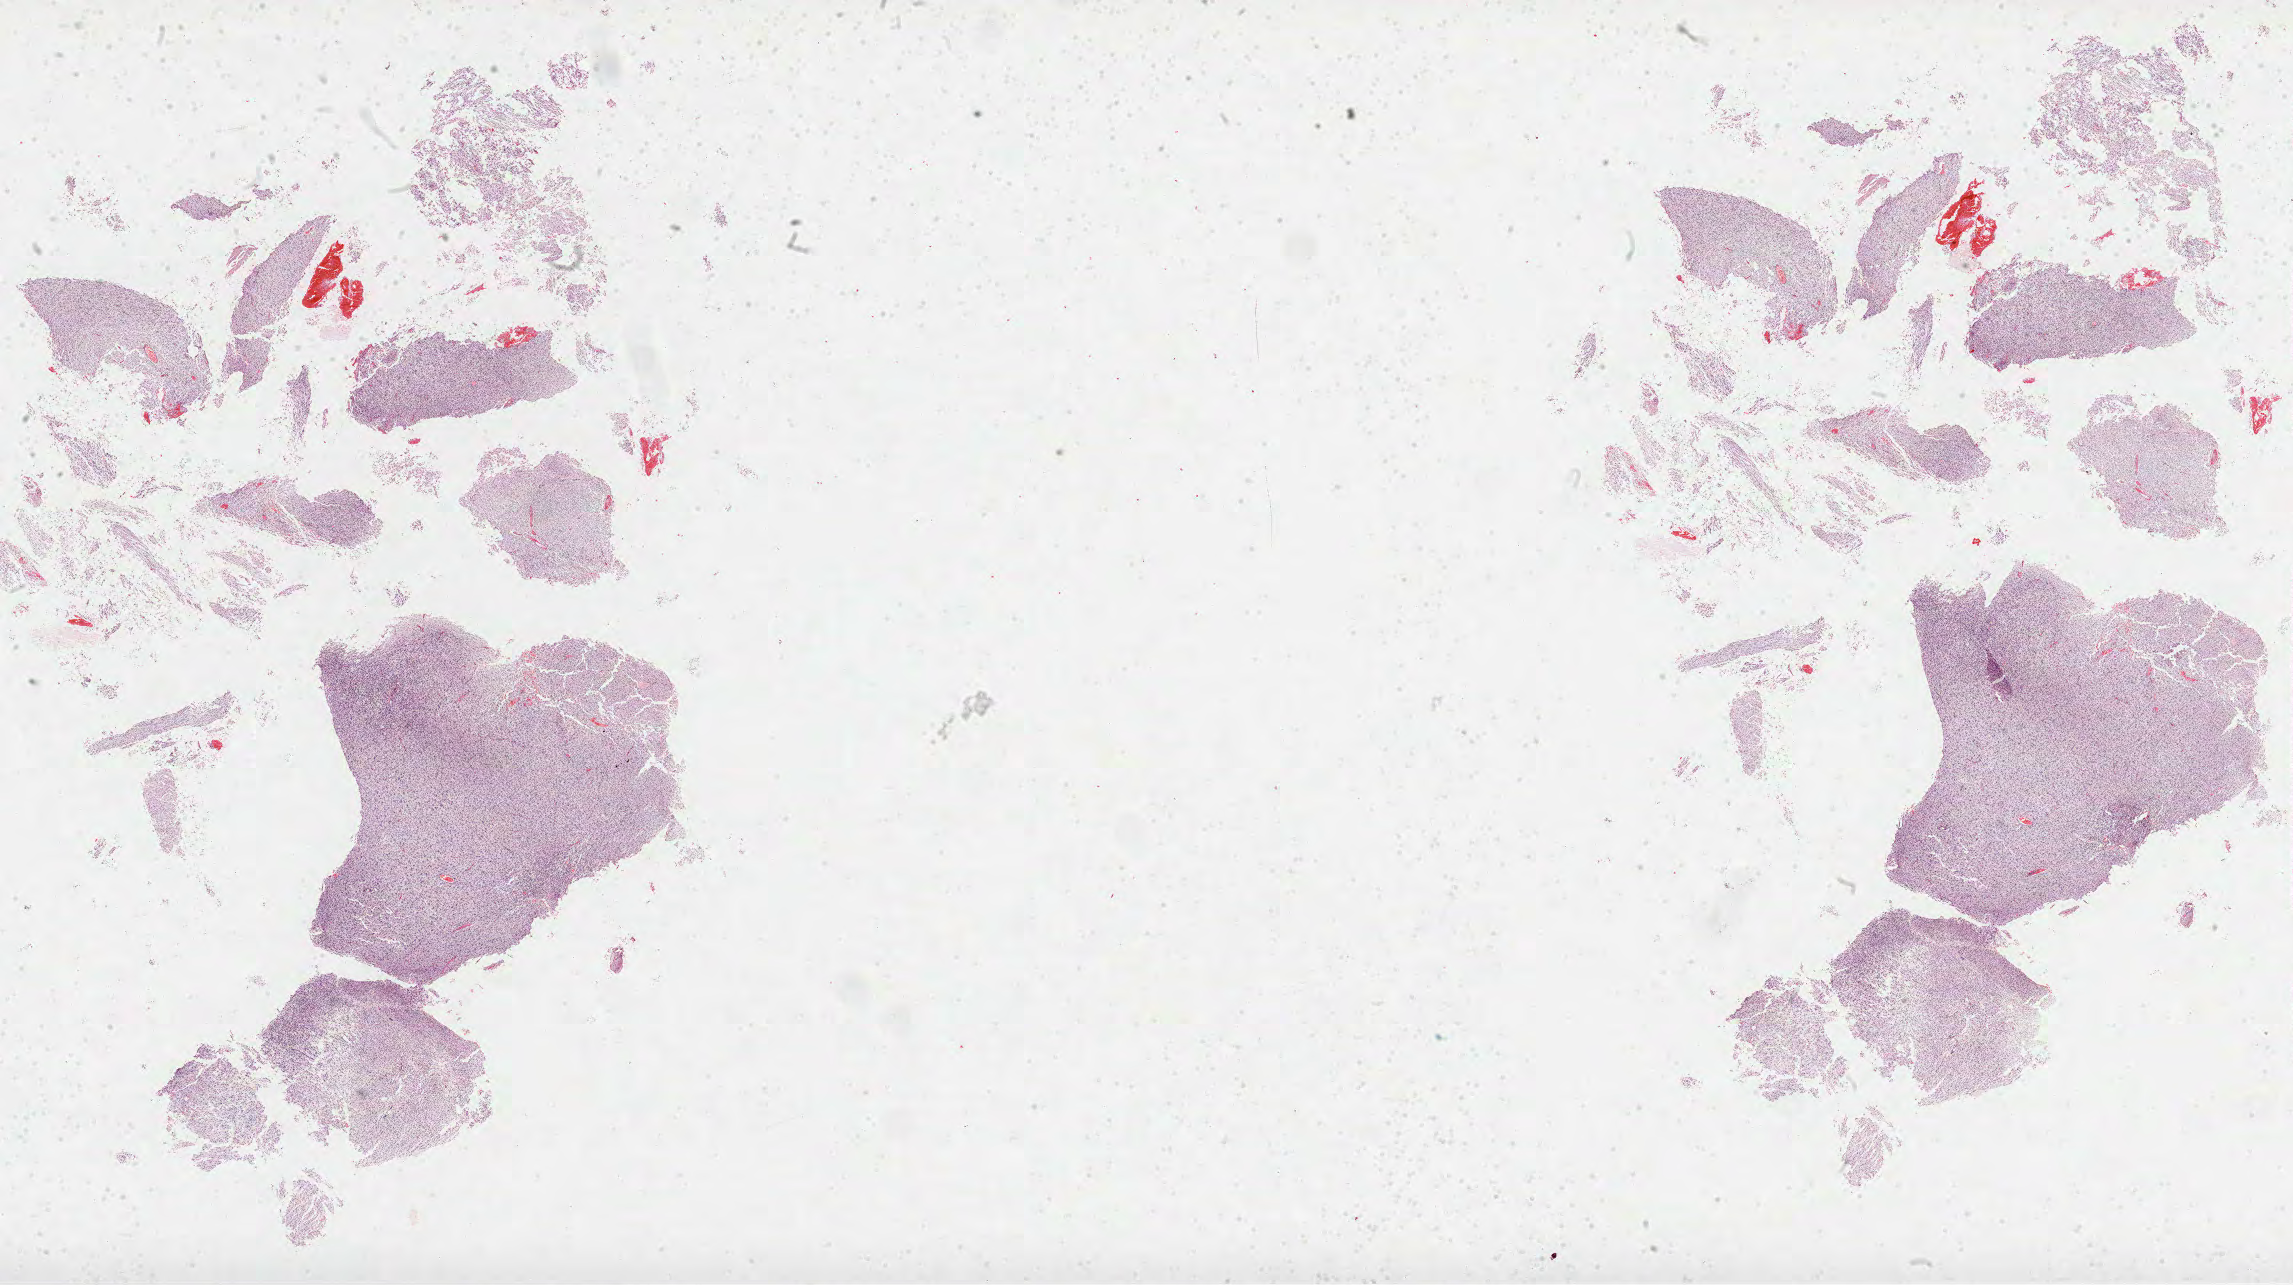
Digitized H&E-stained tissue section (whole slide) — shown as a low-resolution overview of the whole scanned area (about 37.0 x 20.7 mm, acquisition: 40x scan); formalin-fixed paraffin-embedded (FFPE) diagnostic section; primary tumour sample from the brain. Male, age 70 years at initial diagnosis. Histologic grade: G2 (moderately differentiated).
Histologic diagnosis: Oligodendroglioma, NOS (cerebrum).